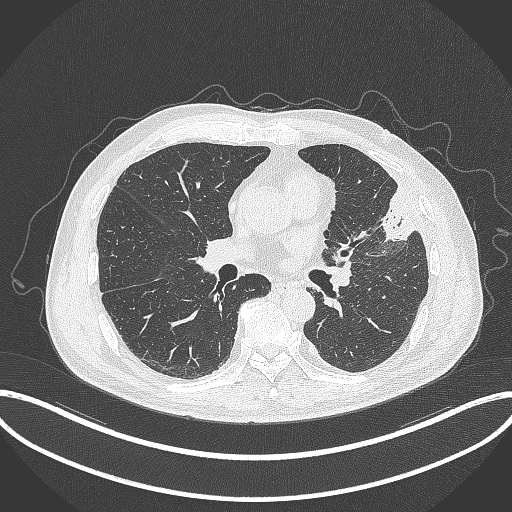
Chest CT, one axial slice. Reconstruction kernel B70f. 120 kVp. Lung window (W 1500 / L -600 HU). 512 × 512 image matrix, field of view 415 × 415 mm. Patient: male, 64 years. Case-level facts recorded for this patient, not image findings: clinical TNM (as recorded): T4 N1 M0.
Outlined on this slice (bounding box drawn by a radiologist):
- lung tumour (recorded histology: adenocarcinoma): bounding box [x1, y1, x2, y2] px = [375, 183, 422, 246]